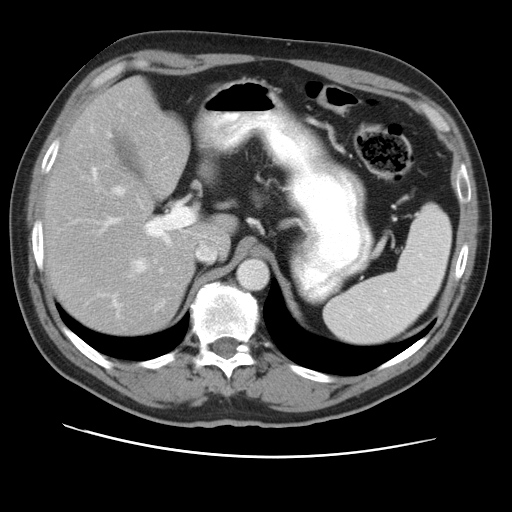
Contrast-enhanced abdominal CT, one axial slice; slice 32 of 49 in the series (ordered by position); reconstruction kernel STANDARD; 120 kVp; soft-tissue window (W 400 / L 40 HU); 5 mm slice thickness; 512 × 512 image matrix, field of view 374 × 374 mm. Male patient, age 59 years. Case-level facts recorded for this patient, not image findings: diagnosis: colorectal cancer liver metastases, imaged before liver resection; multiple liver metastases: yes; largest metastasis: 6.3 cm; disease in both lobes: yes.
Annotated regions visible in this slice (outlined manually by an expert reader):
- hepatic veins: bounding box (x1, y1, x2, y2) in pixels: (115, 187, 216, 272)
- liver: (46, 81, 232, 337)
- planned liver remnant (the part of the liver to remain after resection): (46, 81, 232, 337)
- portal vein (with intrahepatic branches): (76, 166, 195, 308)